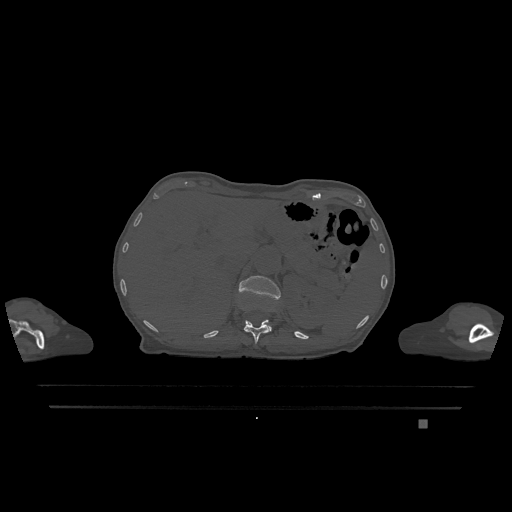
CT including the spine, one axial slice; position 514 of 1317 along the scan axis; bone window (W 1800 / L 400 HU); 512 × 512 image matrix, field of view 500 × 500 mm. Patient: female, 74 years. Case-level facts recorded for this patient, not image findings: primary cancer: lung; vertebrae with lytic lesions (as recorded): T1, T4, T5, T6, L4, L5.
Outlined on this slice (semi-automatic segmentation, software-assisted and operator-edited):
- L1 vertebra: bounding box (x1, y1, x2, y2) in pixels: (239, 275, 281, 331)
- T12 vertebra: (244, 320, 270, 344)